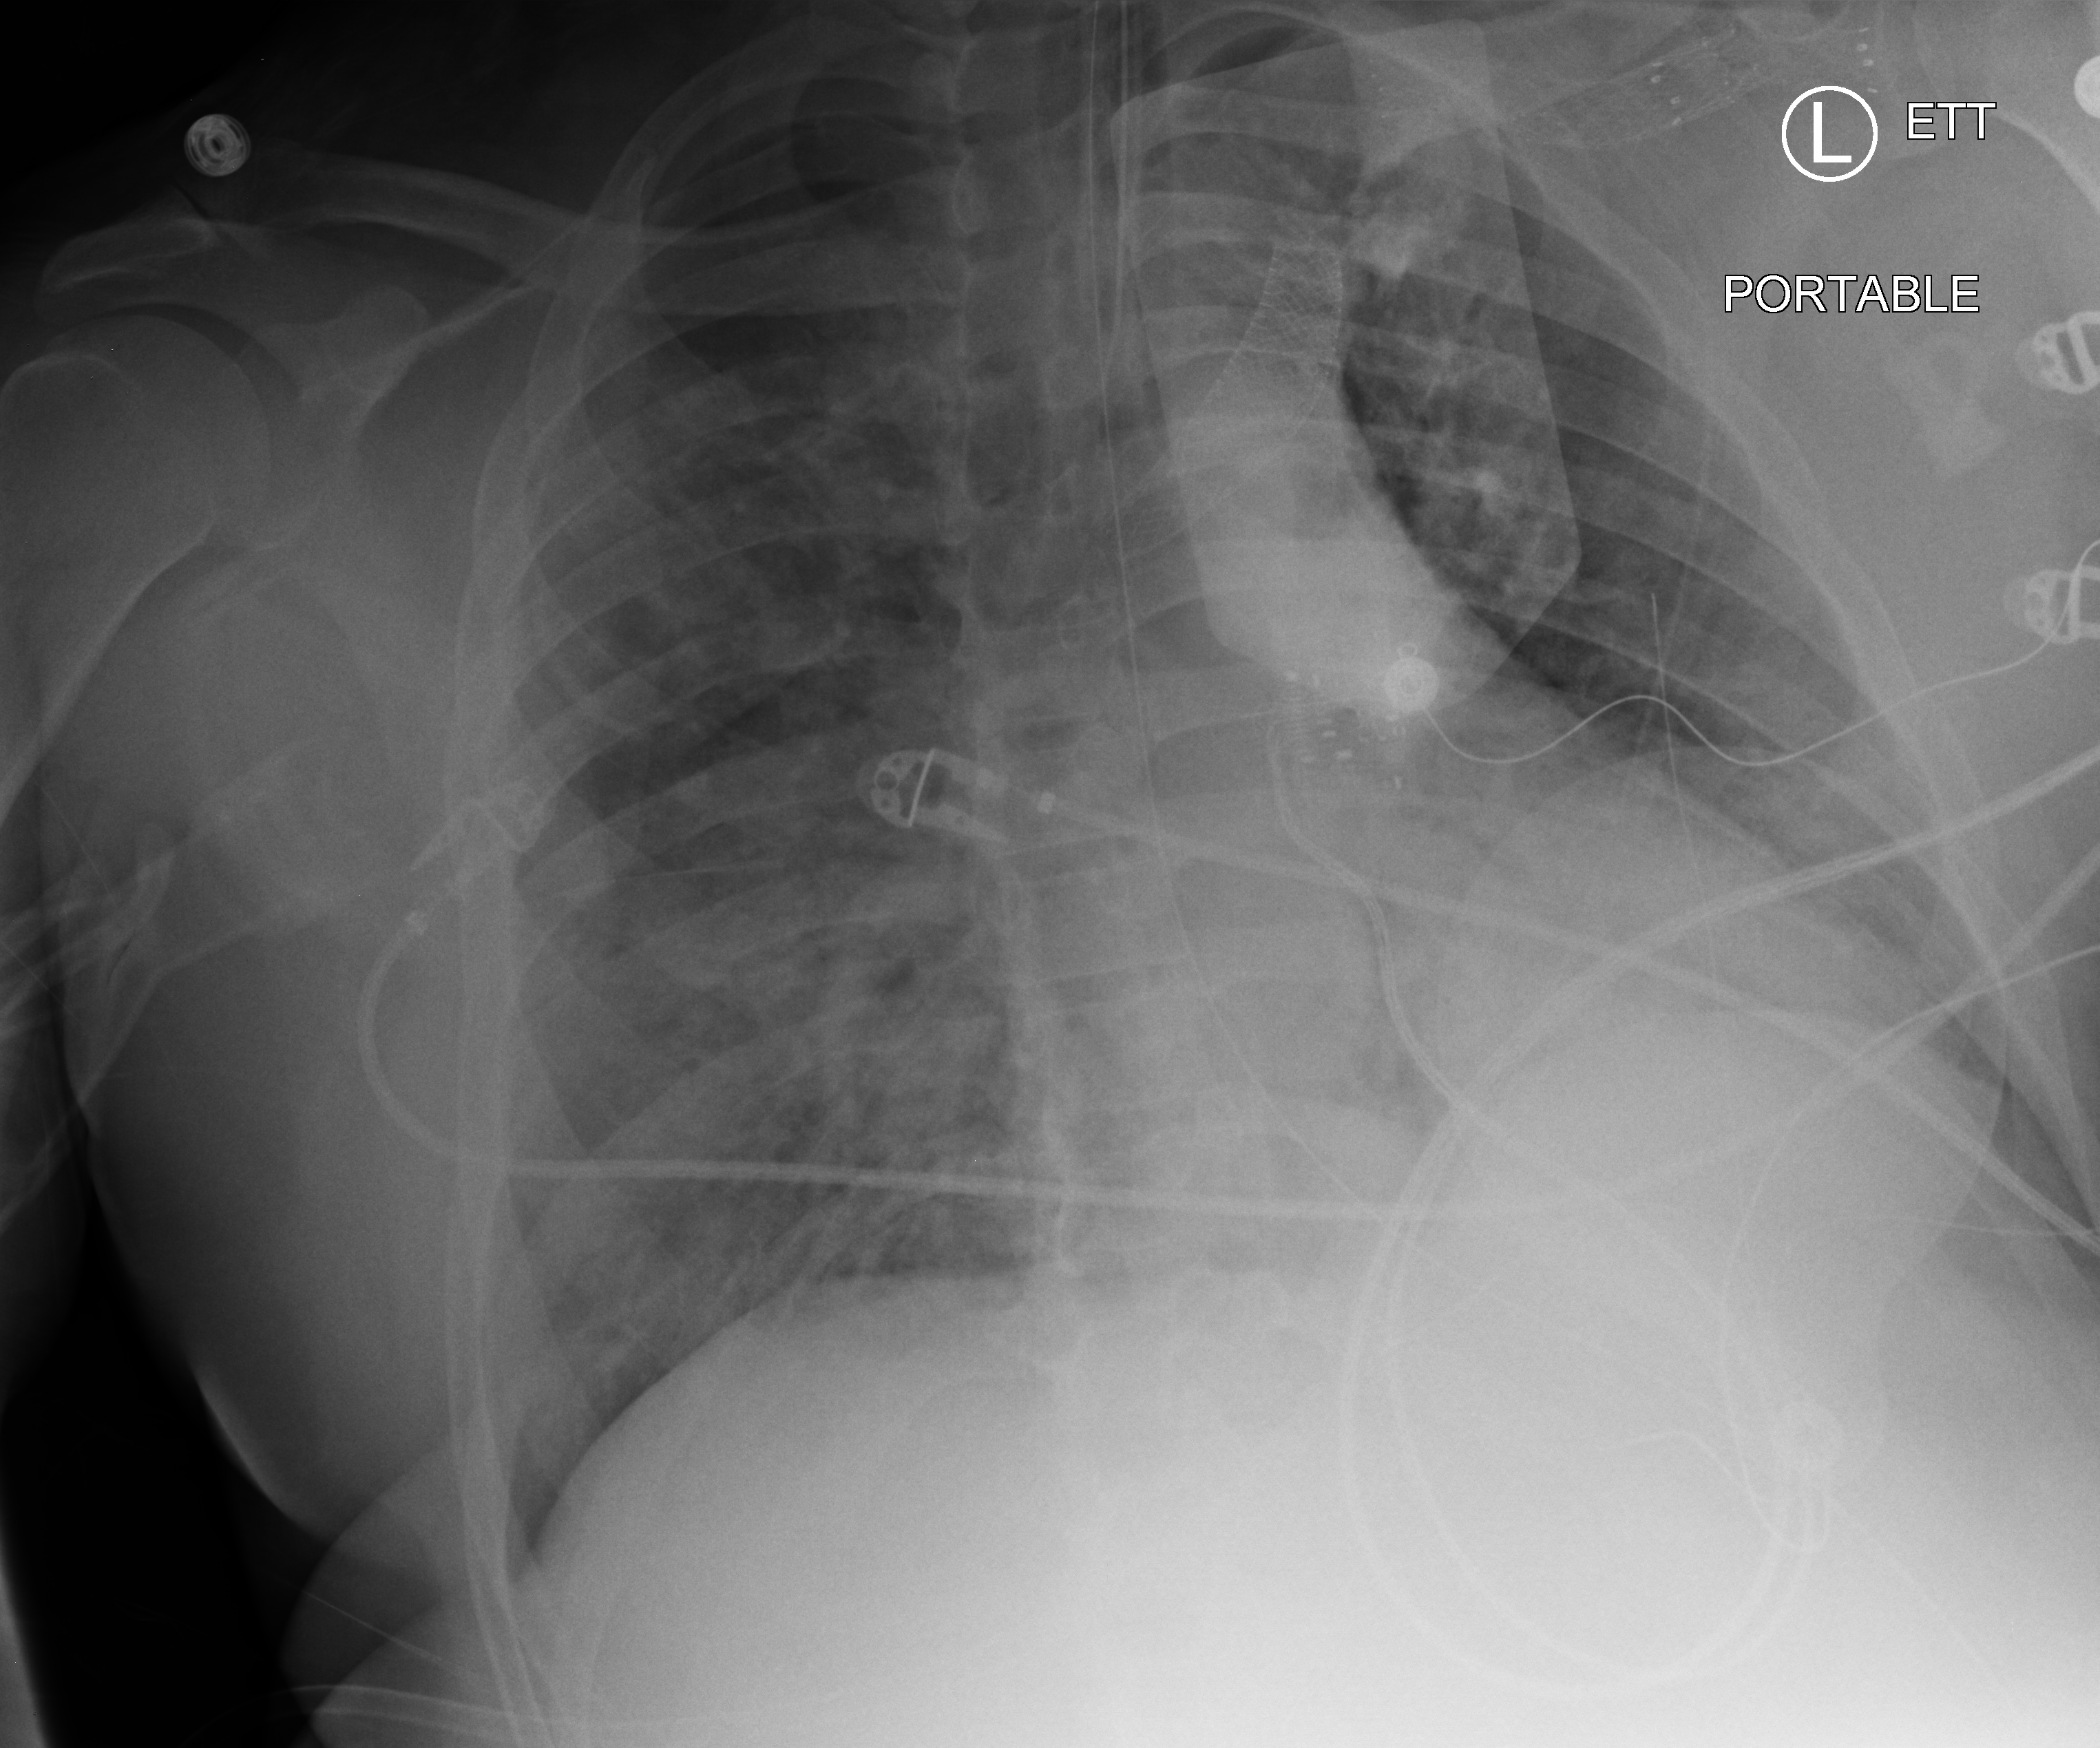
Chest X-ray (portable), anteroposterior (AP) projection. Patient hospitalised with COVID-19; male, aged 18–59 years.
From the hospital-stay record, not from the radiograph (when in the stay this image was taken is not recorded): diabetes (admission record): no.